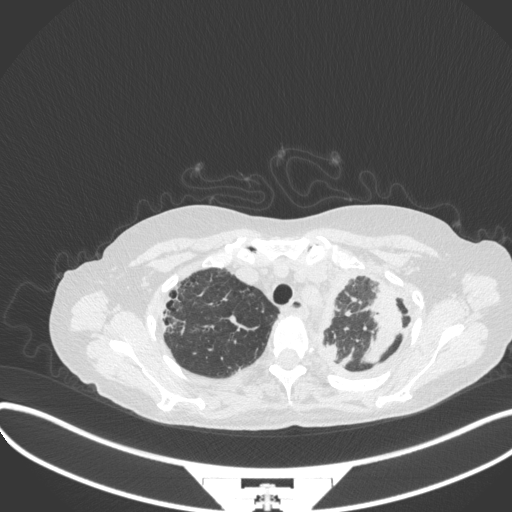
Chest CT, one axial slice. Slice 281 of 373 in the series (ordered by position). Reconstruction kernel B31f. Lung window (W 1500 / L -600 HU). 1 mm slice thickness. 512 × 512 image matrix, field of view 400 × 400 mm. Female patient, age 56 years. Case-level facts recorded for this patient, not image findings: clinical TNM (as recorded): T1 N0 M0.
Outlined on this slice (rectangle marked by the reading radiologist):
- lung tumour (recorded histology: adenocarcinoma): bounding box [x1, y1, x2, y2] px = [364, 281, 403, 365]